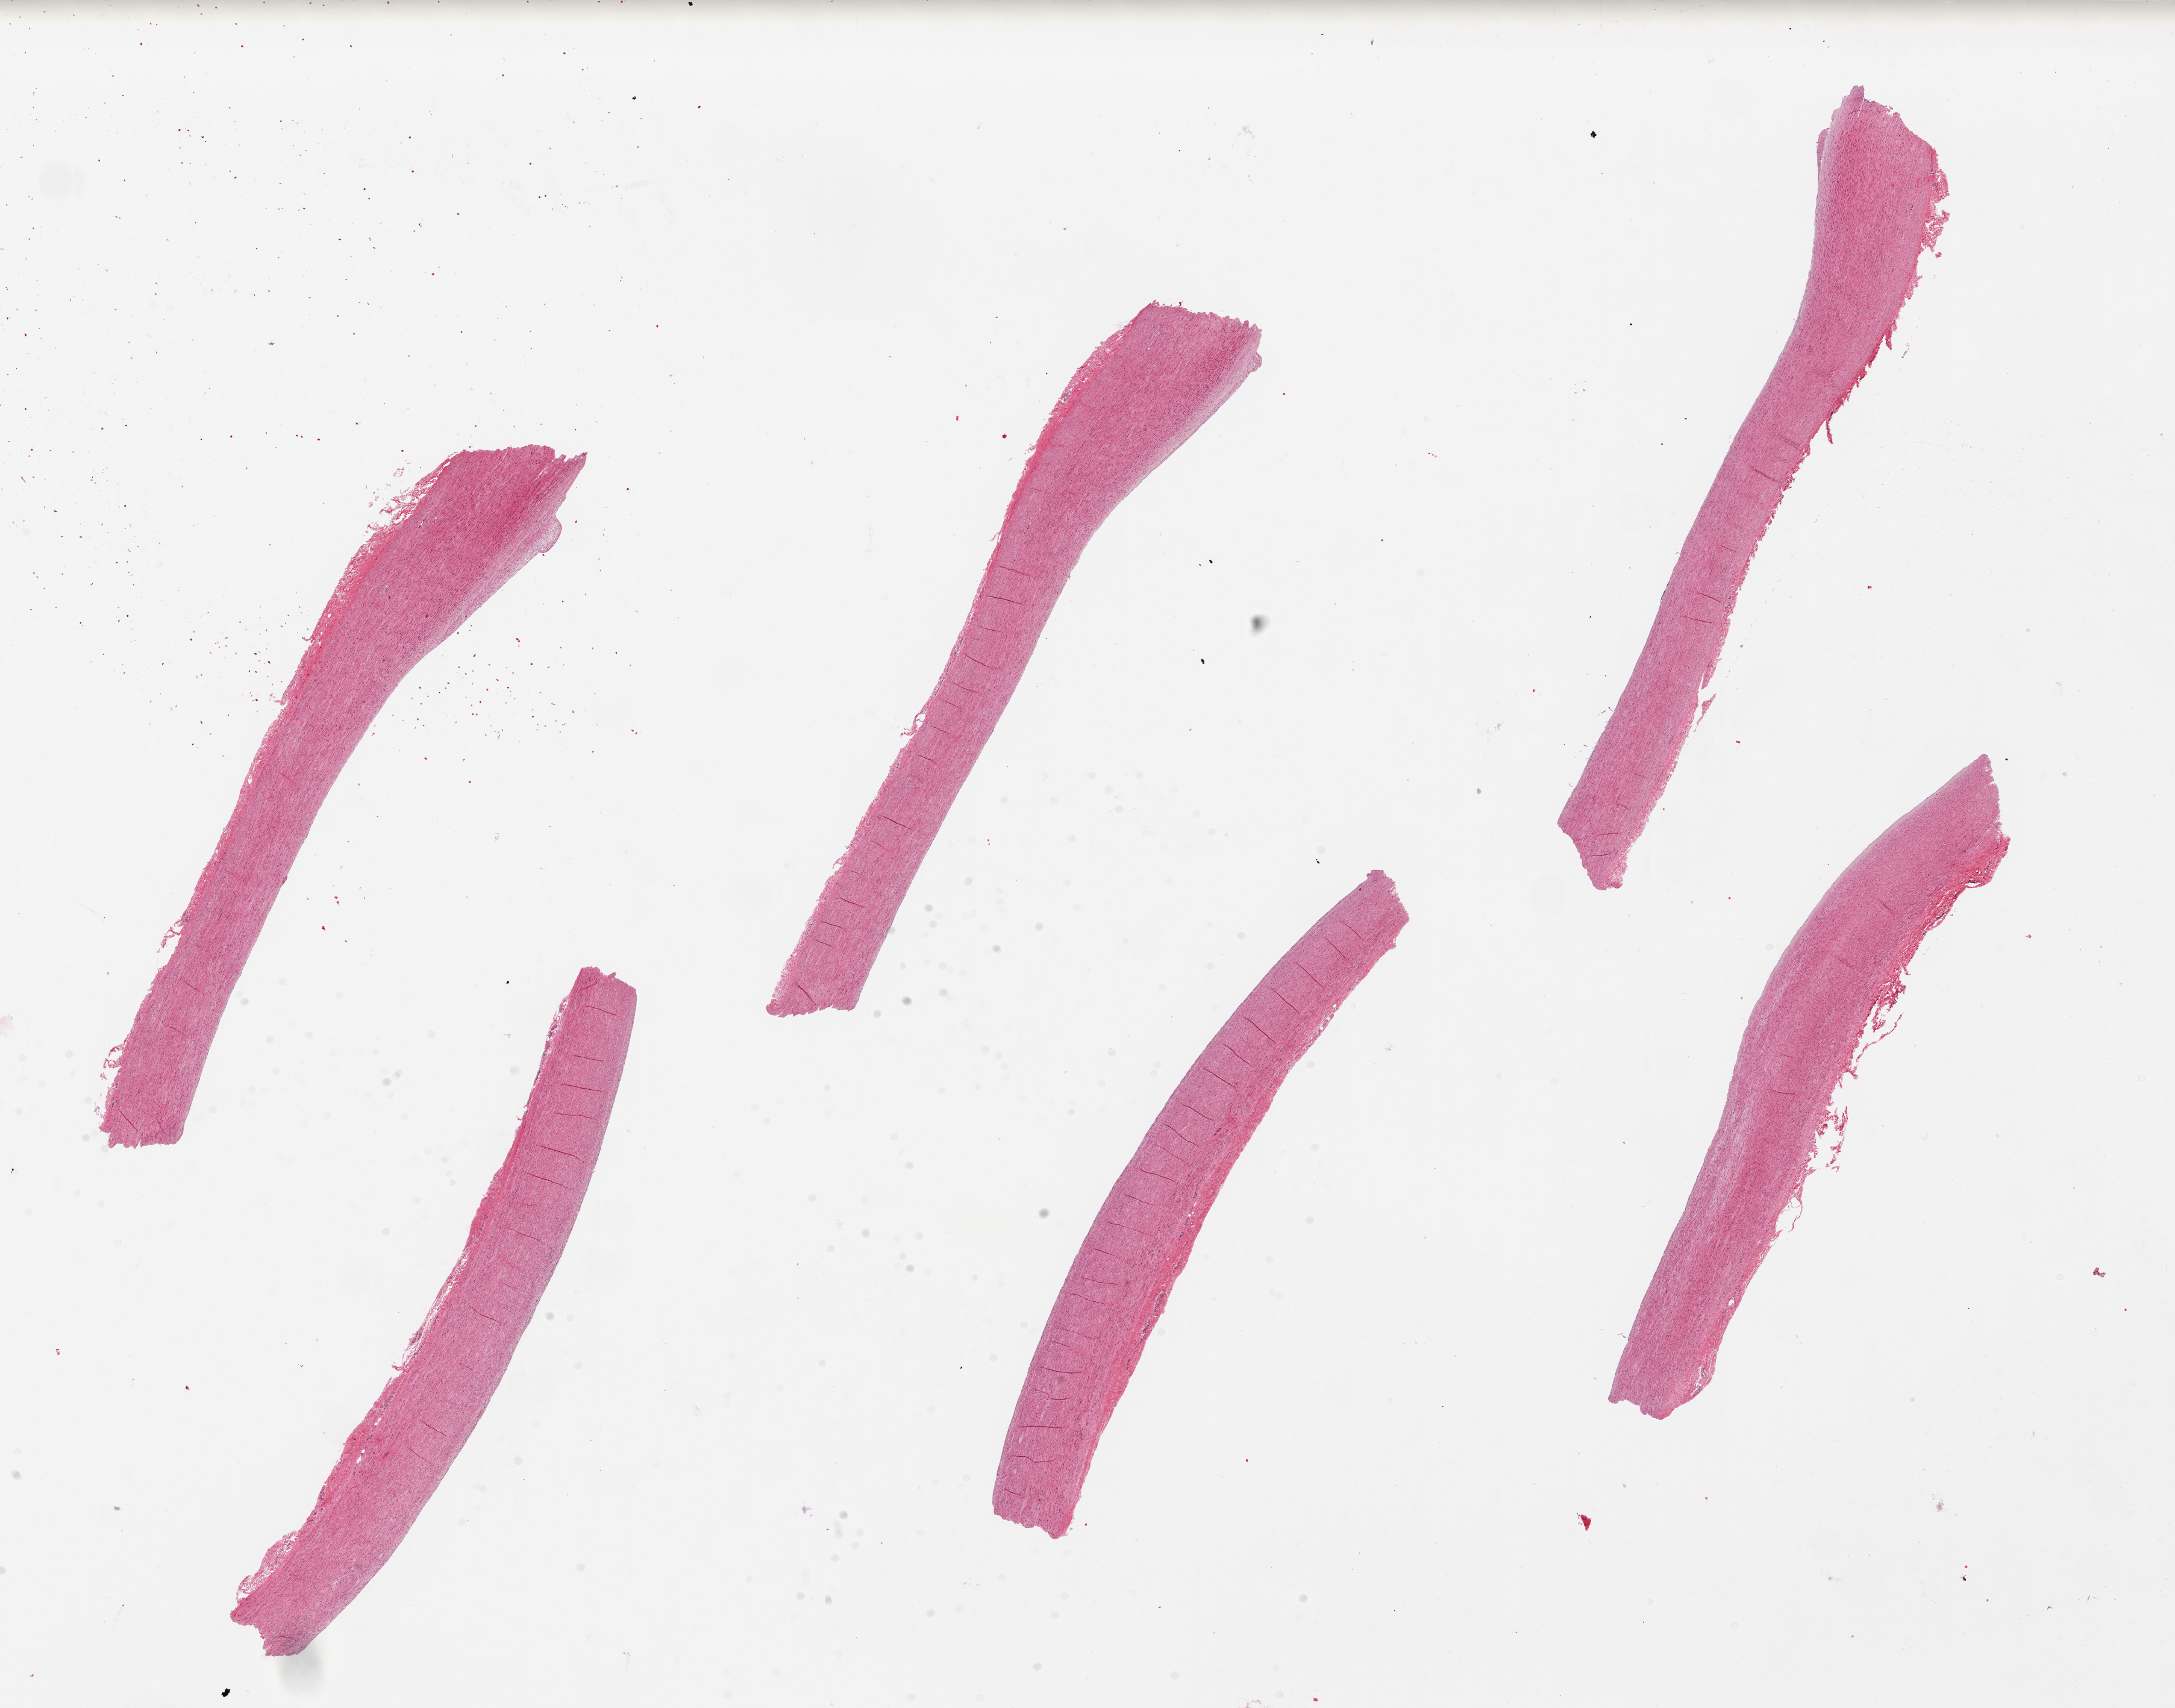
Whole-slide image, hematoxylin and eosin (H&E) stain, brightfield, a low-resolution overview of the entire scanned area, about 28.5 x 22.4 mm; PAXgene-fixed, paraffin-embedded tissue; sampled site (target tissue): aorta; tissue donor sample. Donor: male.
Pathologist's review note for this sample: 6 pieces. up to 11x2mm; Well trimmed. Only 1 small plaque.